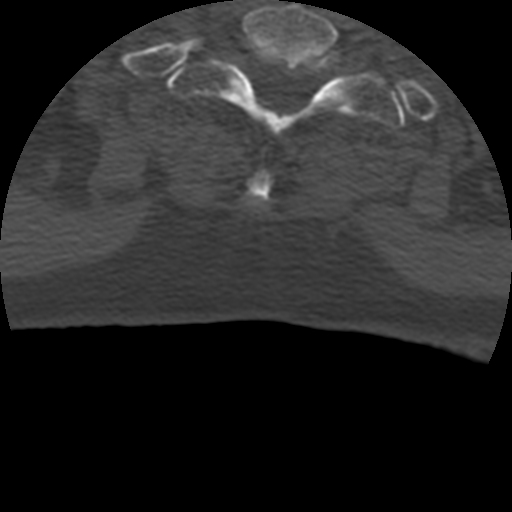
CT including the spine, one axial slice. Slice 387 of 399 in the series (ordered by position). Reconstruction kernel STANDARD. Bone window (W 1800 / L 400 HU). 512 × 512 image matrix, field of view 160 × 160 mm. Patient age 69 years. From the clinical record (not read from this slice): primary cancer: prostate.
Outlined on this slice (semi-automatically segmented with operator editing):
- T1 vertebra: bounding box [x1, y1, x2, y2] px = [169, 37, 405, 139]